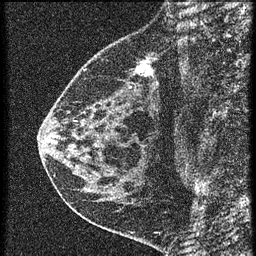
Breast MRI (dynamic contrast-enhanced), one sagittal slice; slice 21 of 60 in the series (ordered by position); 3 images stored at this slice position (order not interpretable as contrast timing); 1.5 T; TE 4.2 ms, TR 20.4 ms; 256 × 256 image matrix. Female patient, age 46 years. Case-level facts recorded for this patient, not image findings: setting: breast cancer imaged before/during neoadjuvant chemotherapy; receptor status: HR-positive, HER2-negative.
Annotated regions visible in this slice (semi-automatic segmentation, software-assisted and operator-edited):
- analysis volume of interest (the breast-tissue region the enhancement analysis was run in; not a lesion): bounding box (x1, y1, x2, y2) in pixels: (58, 36, 167, 155)
- tumour enhancement mask (voxels above the 90 % enhancement threshold inside the analysis volume of interest): (138, 64, 151, 75)